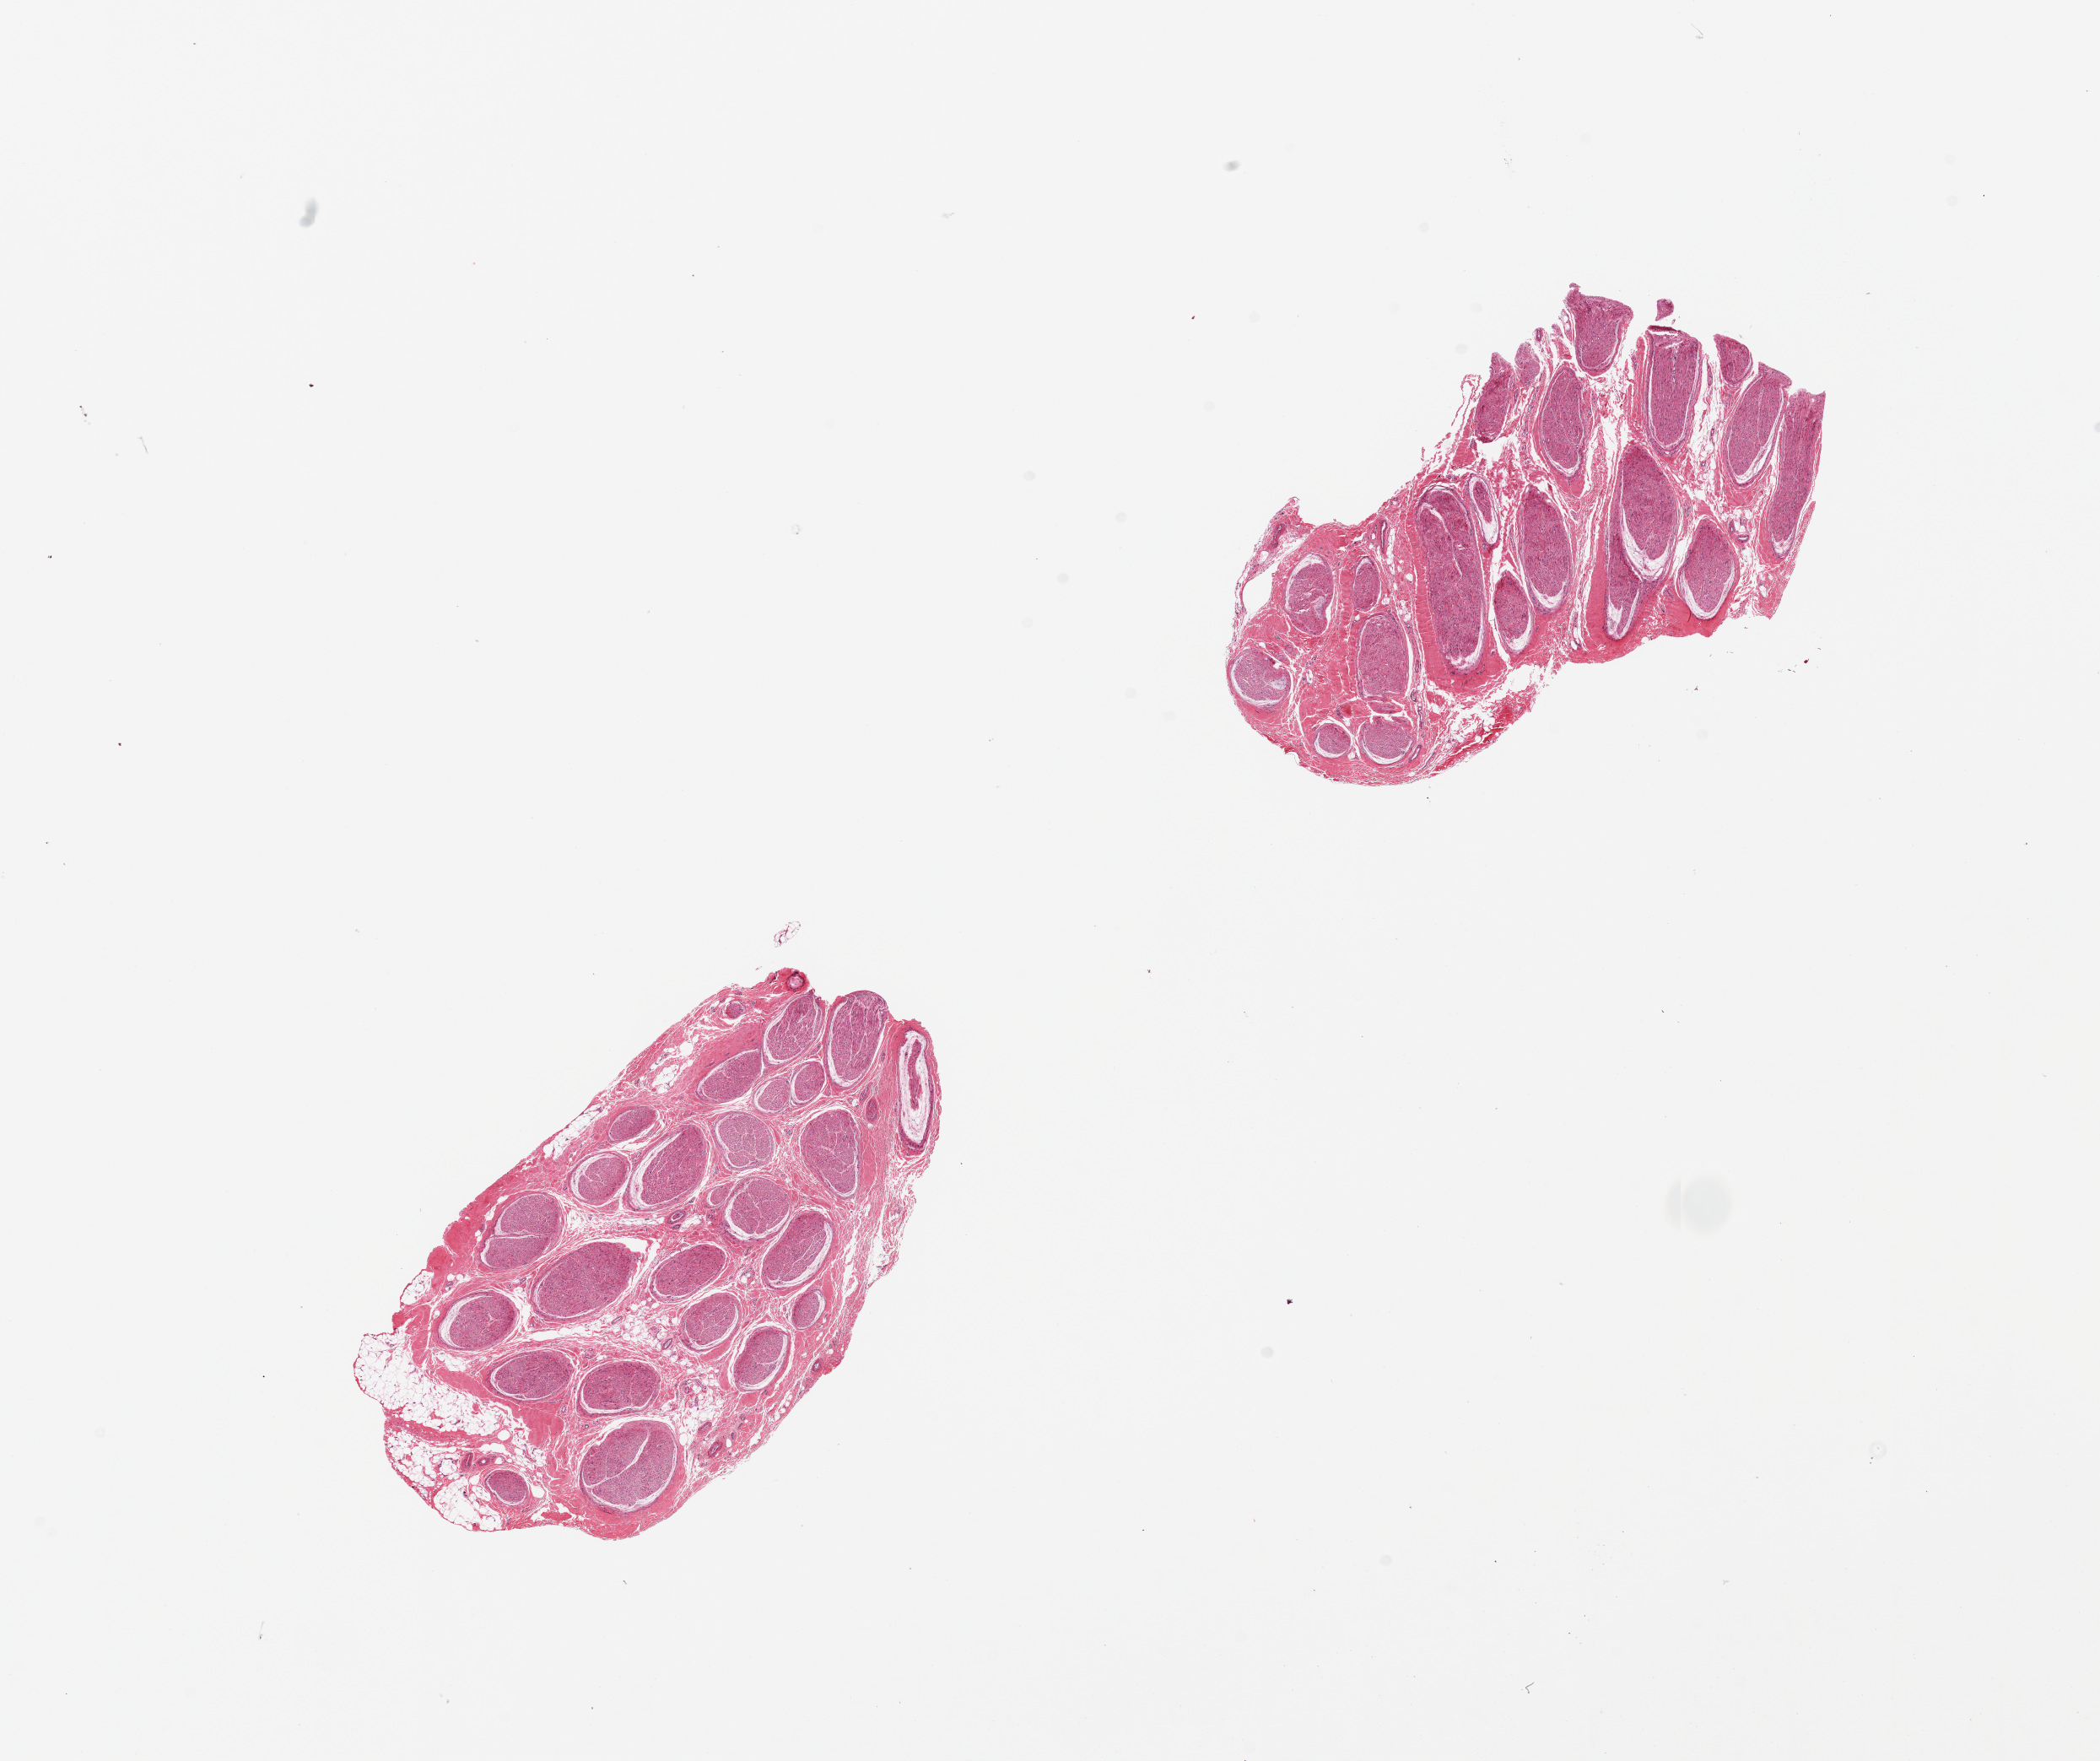
Haematoxylin and eosin whole-slide image, low-resolution overview of the scanned area, about 19.7 x 16.5 mm, PAXgene-fixed paraffin-embedded (PFPE) section, sampled site (target tissue): tibial nerve, donor tissue sample. Male donor.
Reviewer comment on this tissue sample: 2 pieces. well trimmed.